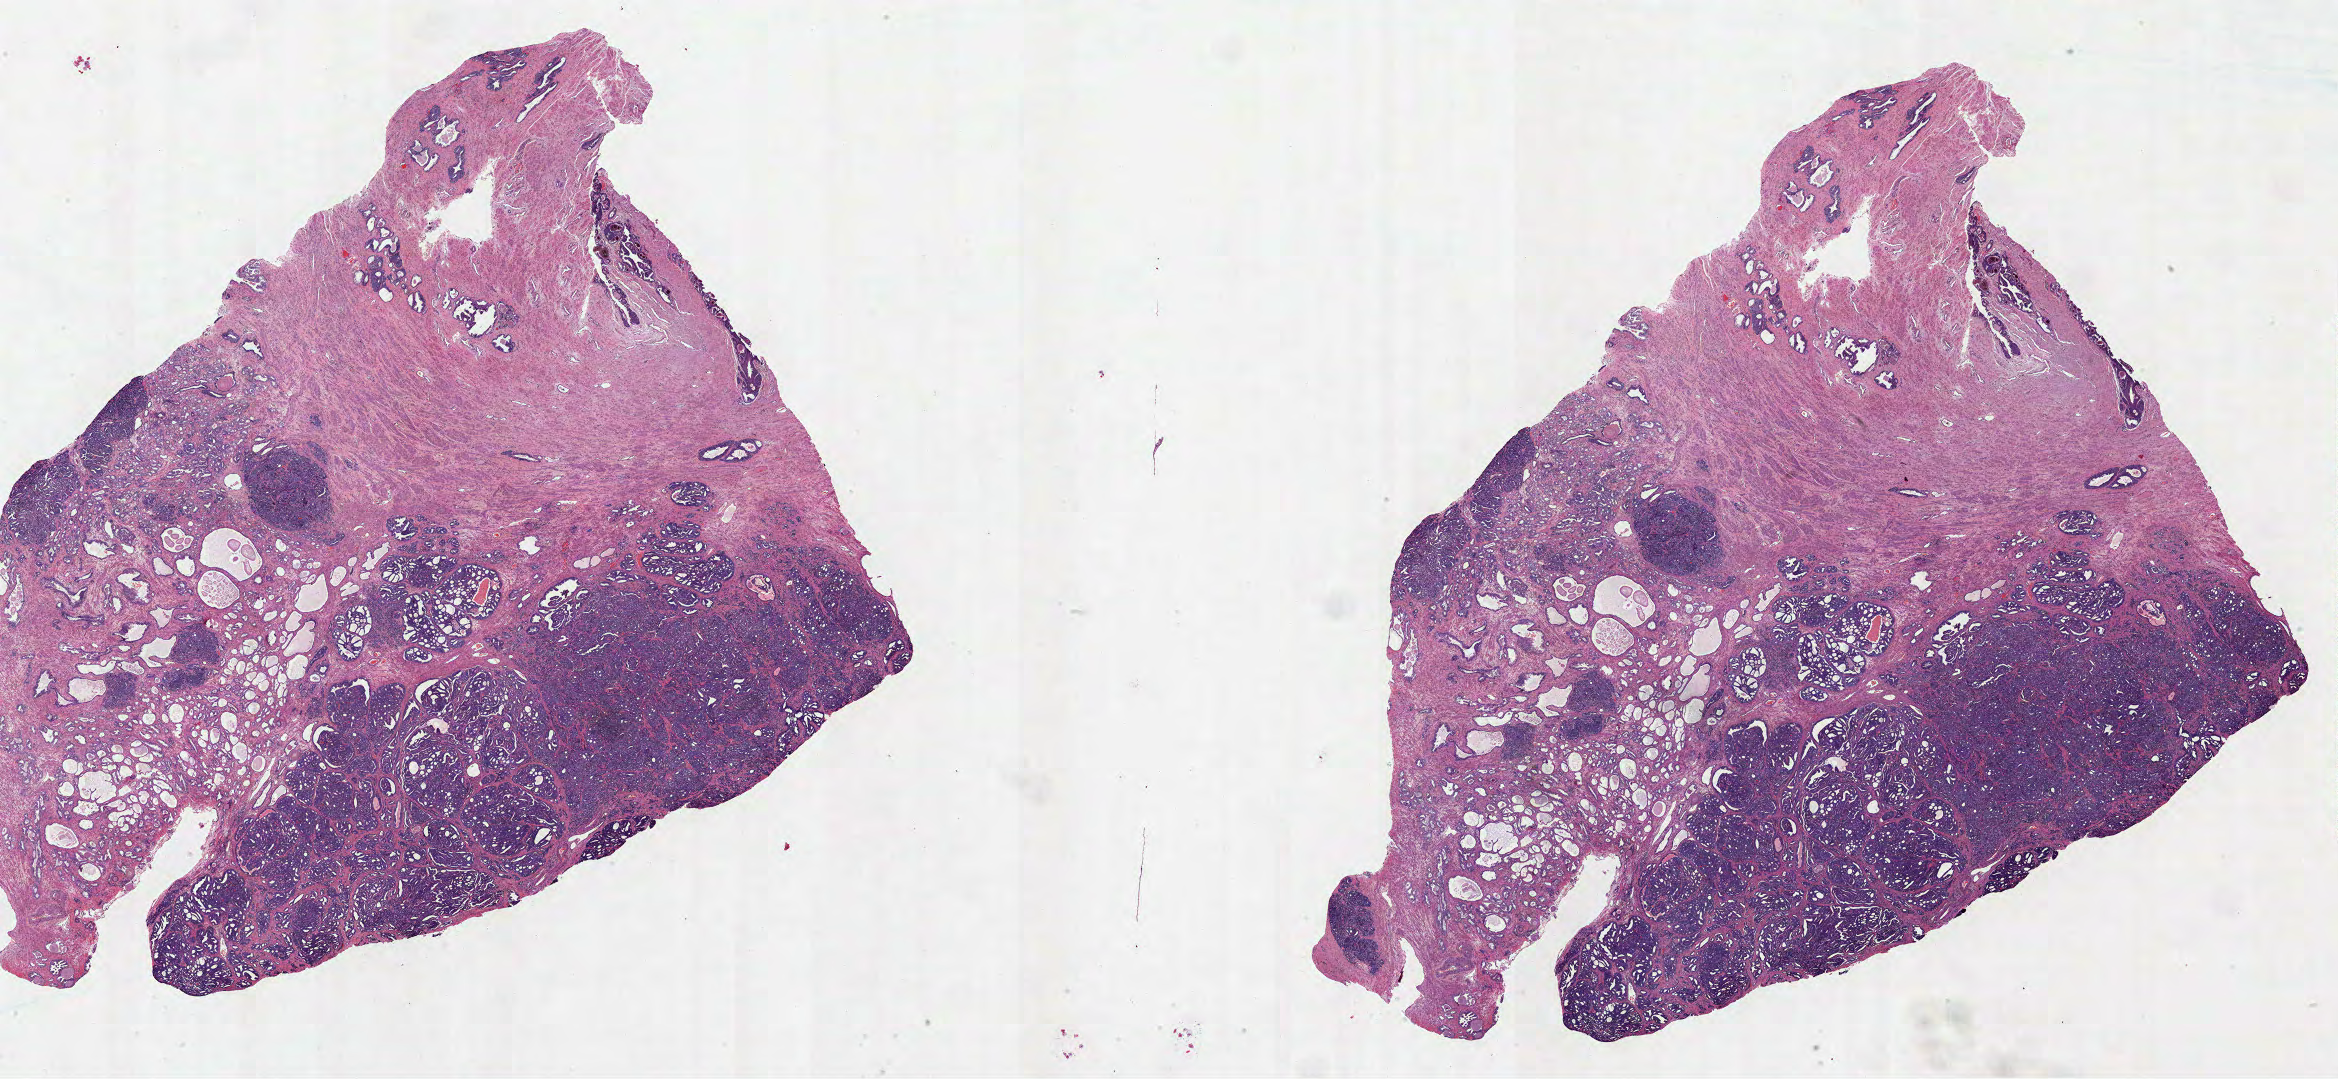
Whole-slide histology image, Hematoxylin and eosin (H&E) stained — low-resolution overview of the scanned area, about 37.7 x 17.4 mm; FFPE section; prostate, primary tumour sample. Male patient; age at initial diagnosis 70 years. Gleason score: 7 (4+3).
Pathologic diagnosis: Acinar cell carcinoma. Lymph nodes positive (case pathology): 0 of 17 examined. Laterality: bilateral.